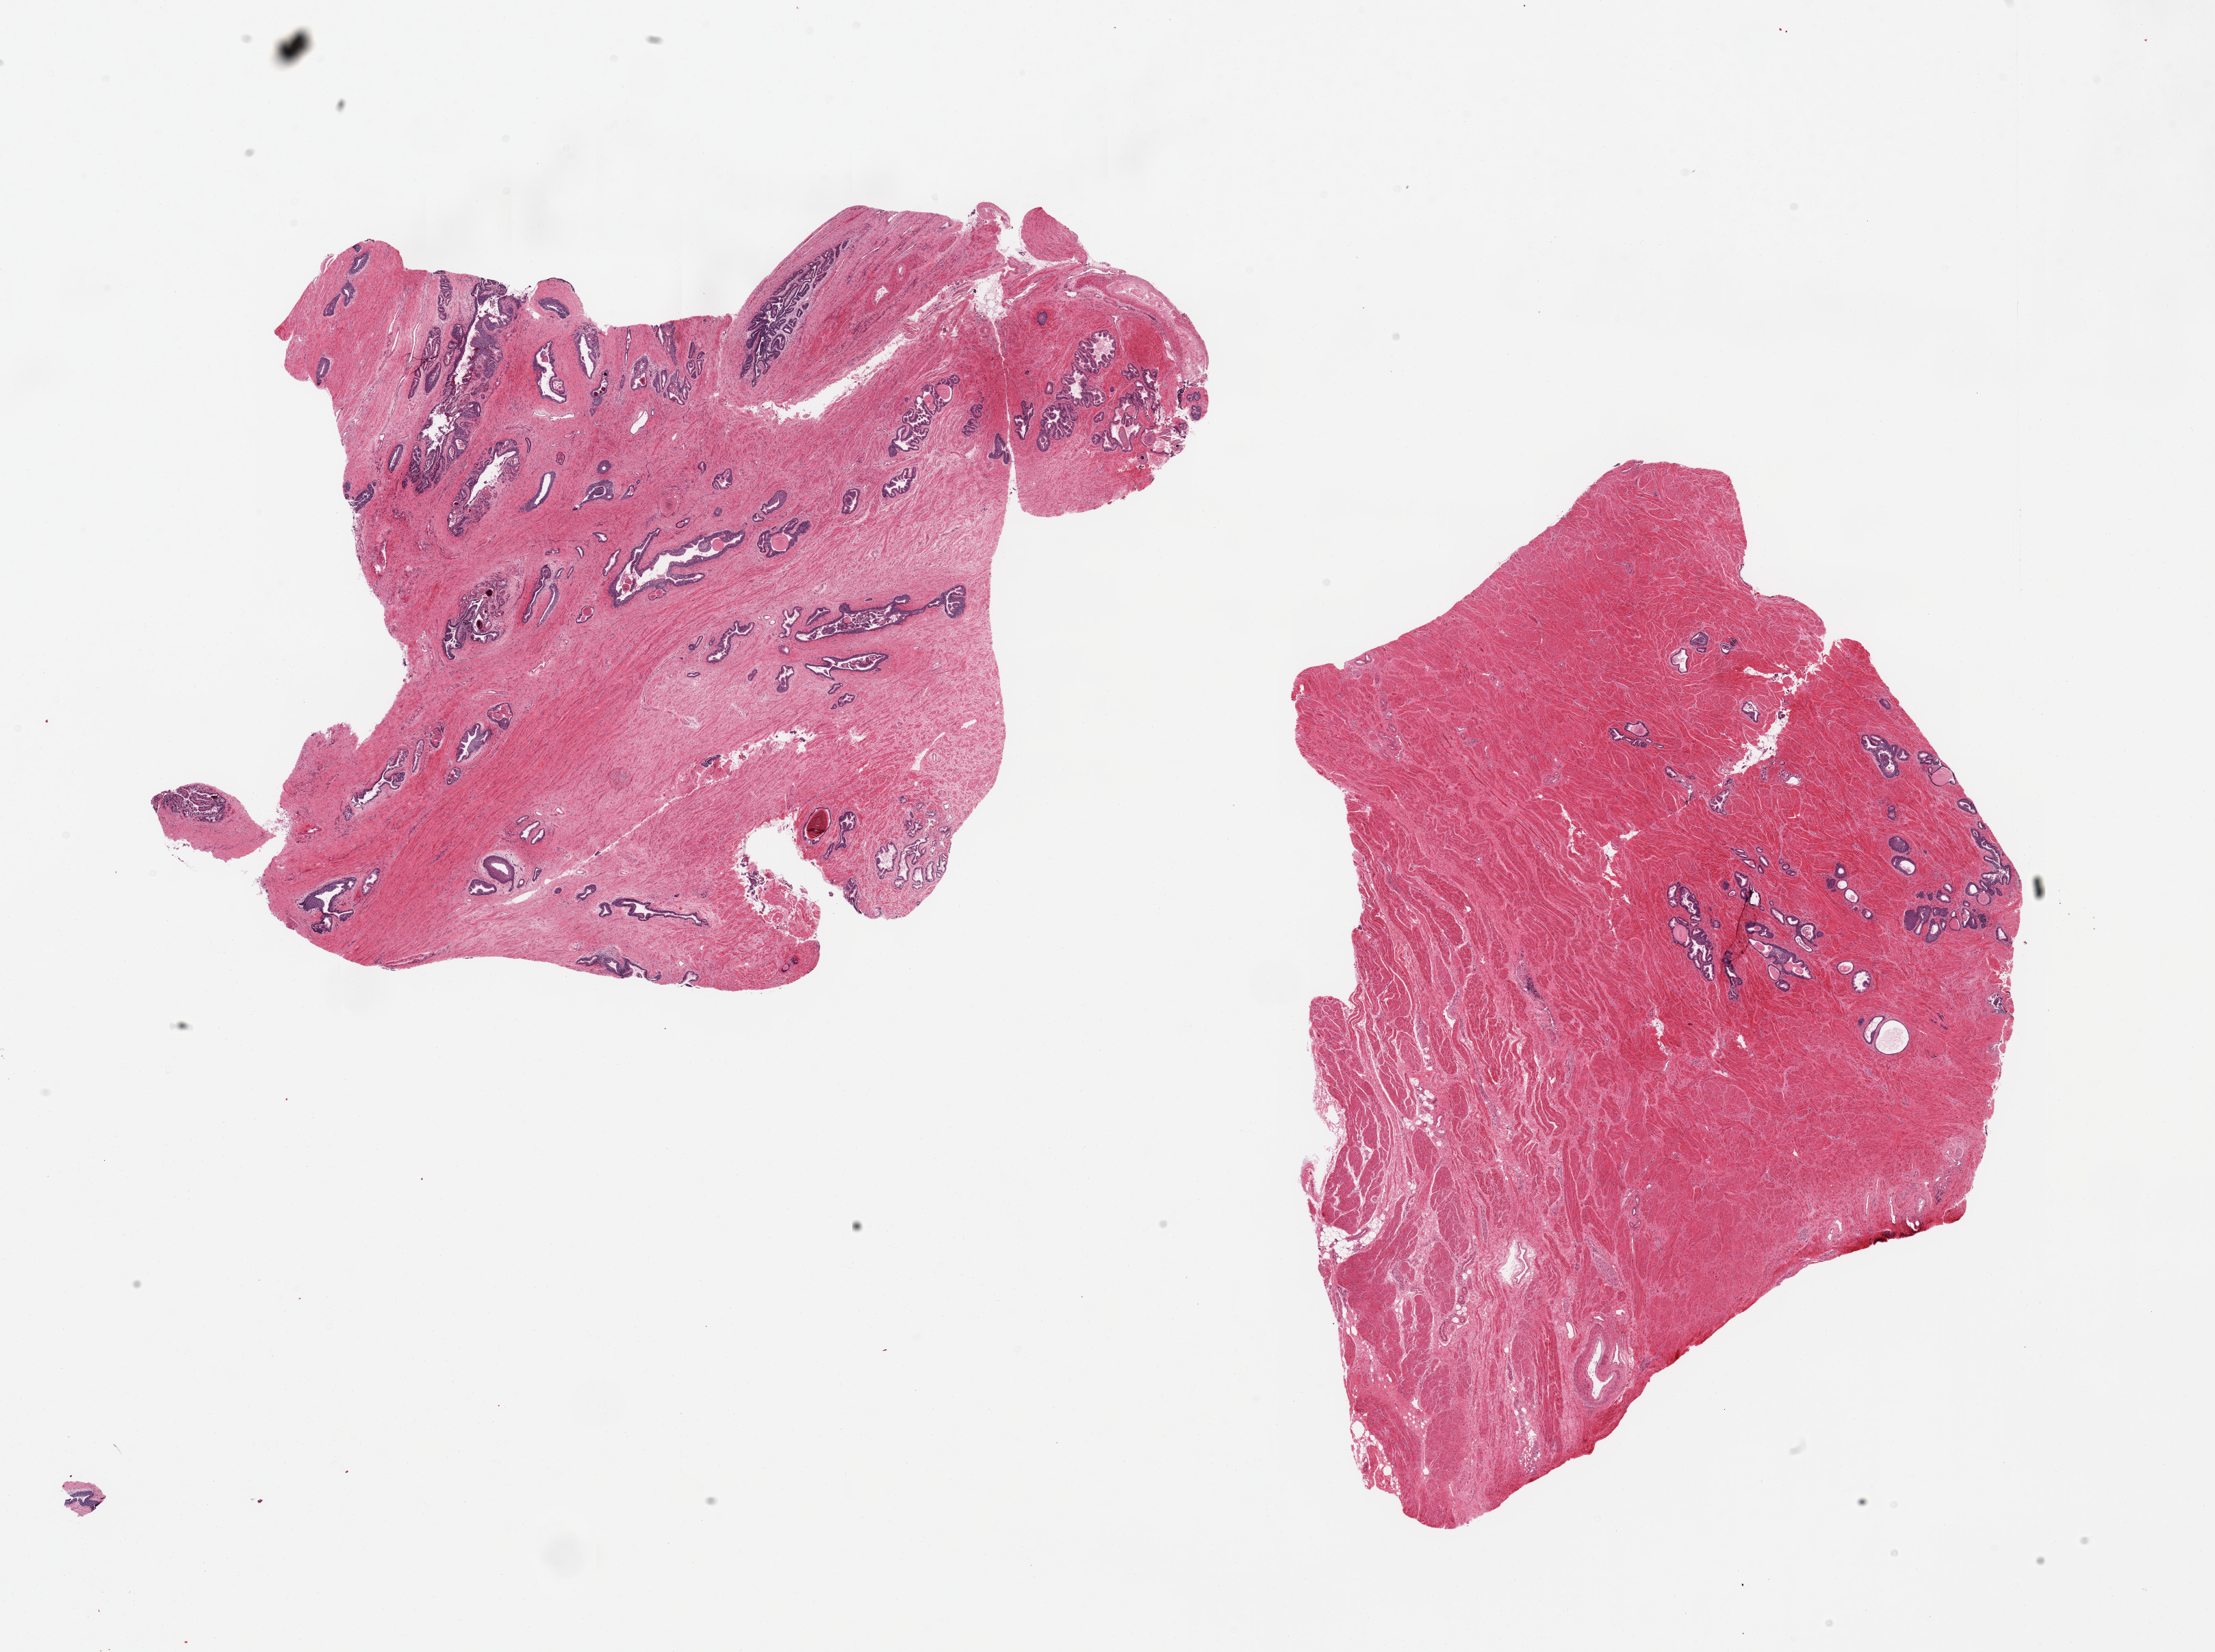
H&E whole-slide image — shown as a low-resolution overview of the whole scanned area (about 25.6 x 19.1 mm, acquisition: 20x scan), PAXgene-fixed, paraffin-embedded tissue, sampled site (target tissue): prostate, donor tissue sample.
- review note (as recorded): 2 pieces; 1 shows stromal fibrosis, numerous corpora amylacea; second piece consists of 25% glandular component and 75% fibromuscular stroma